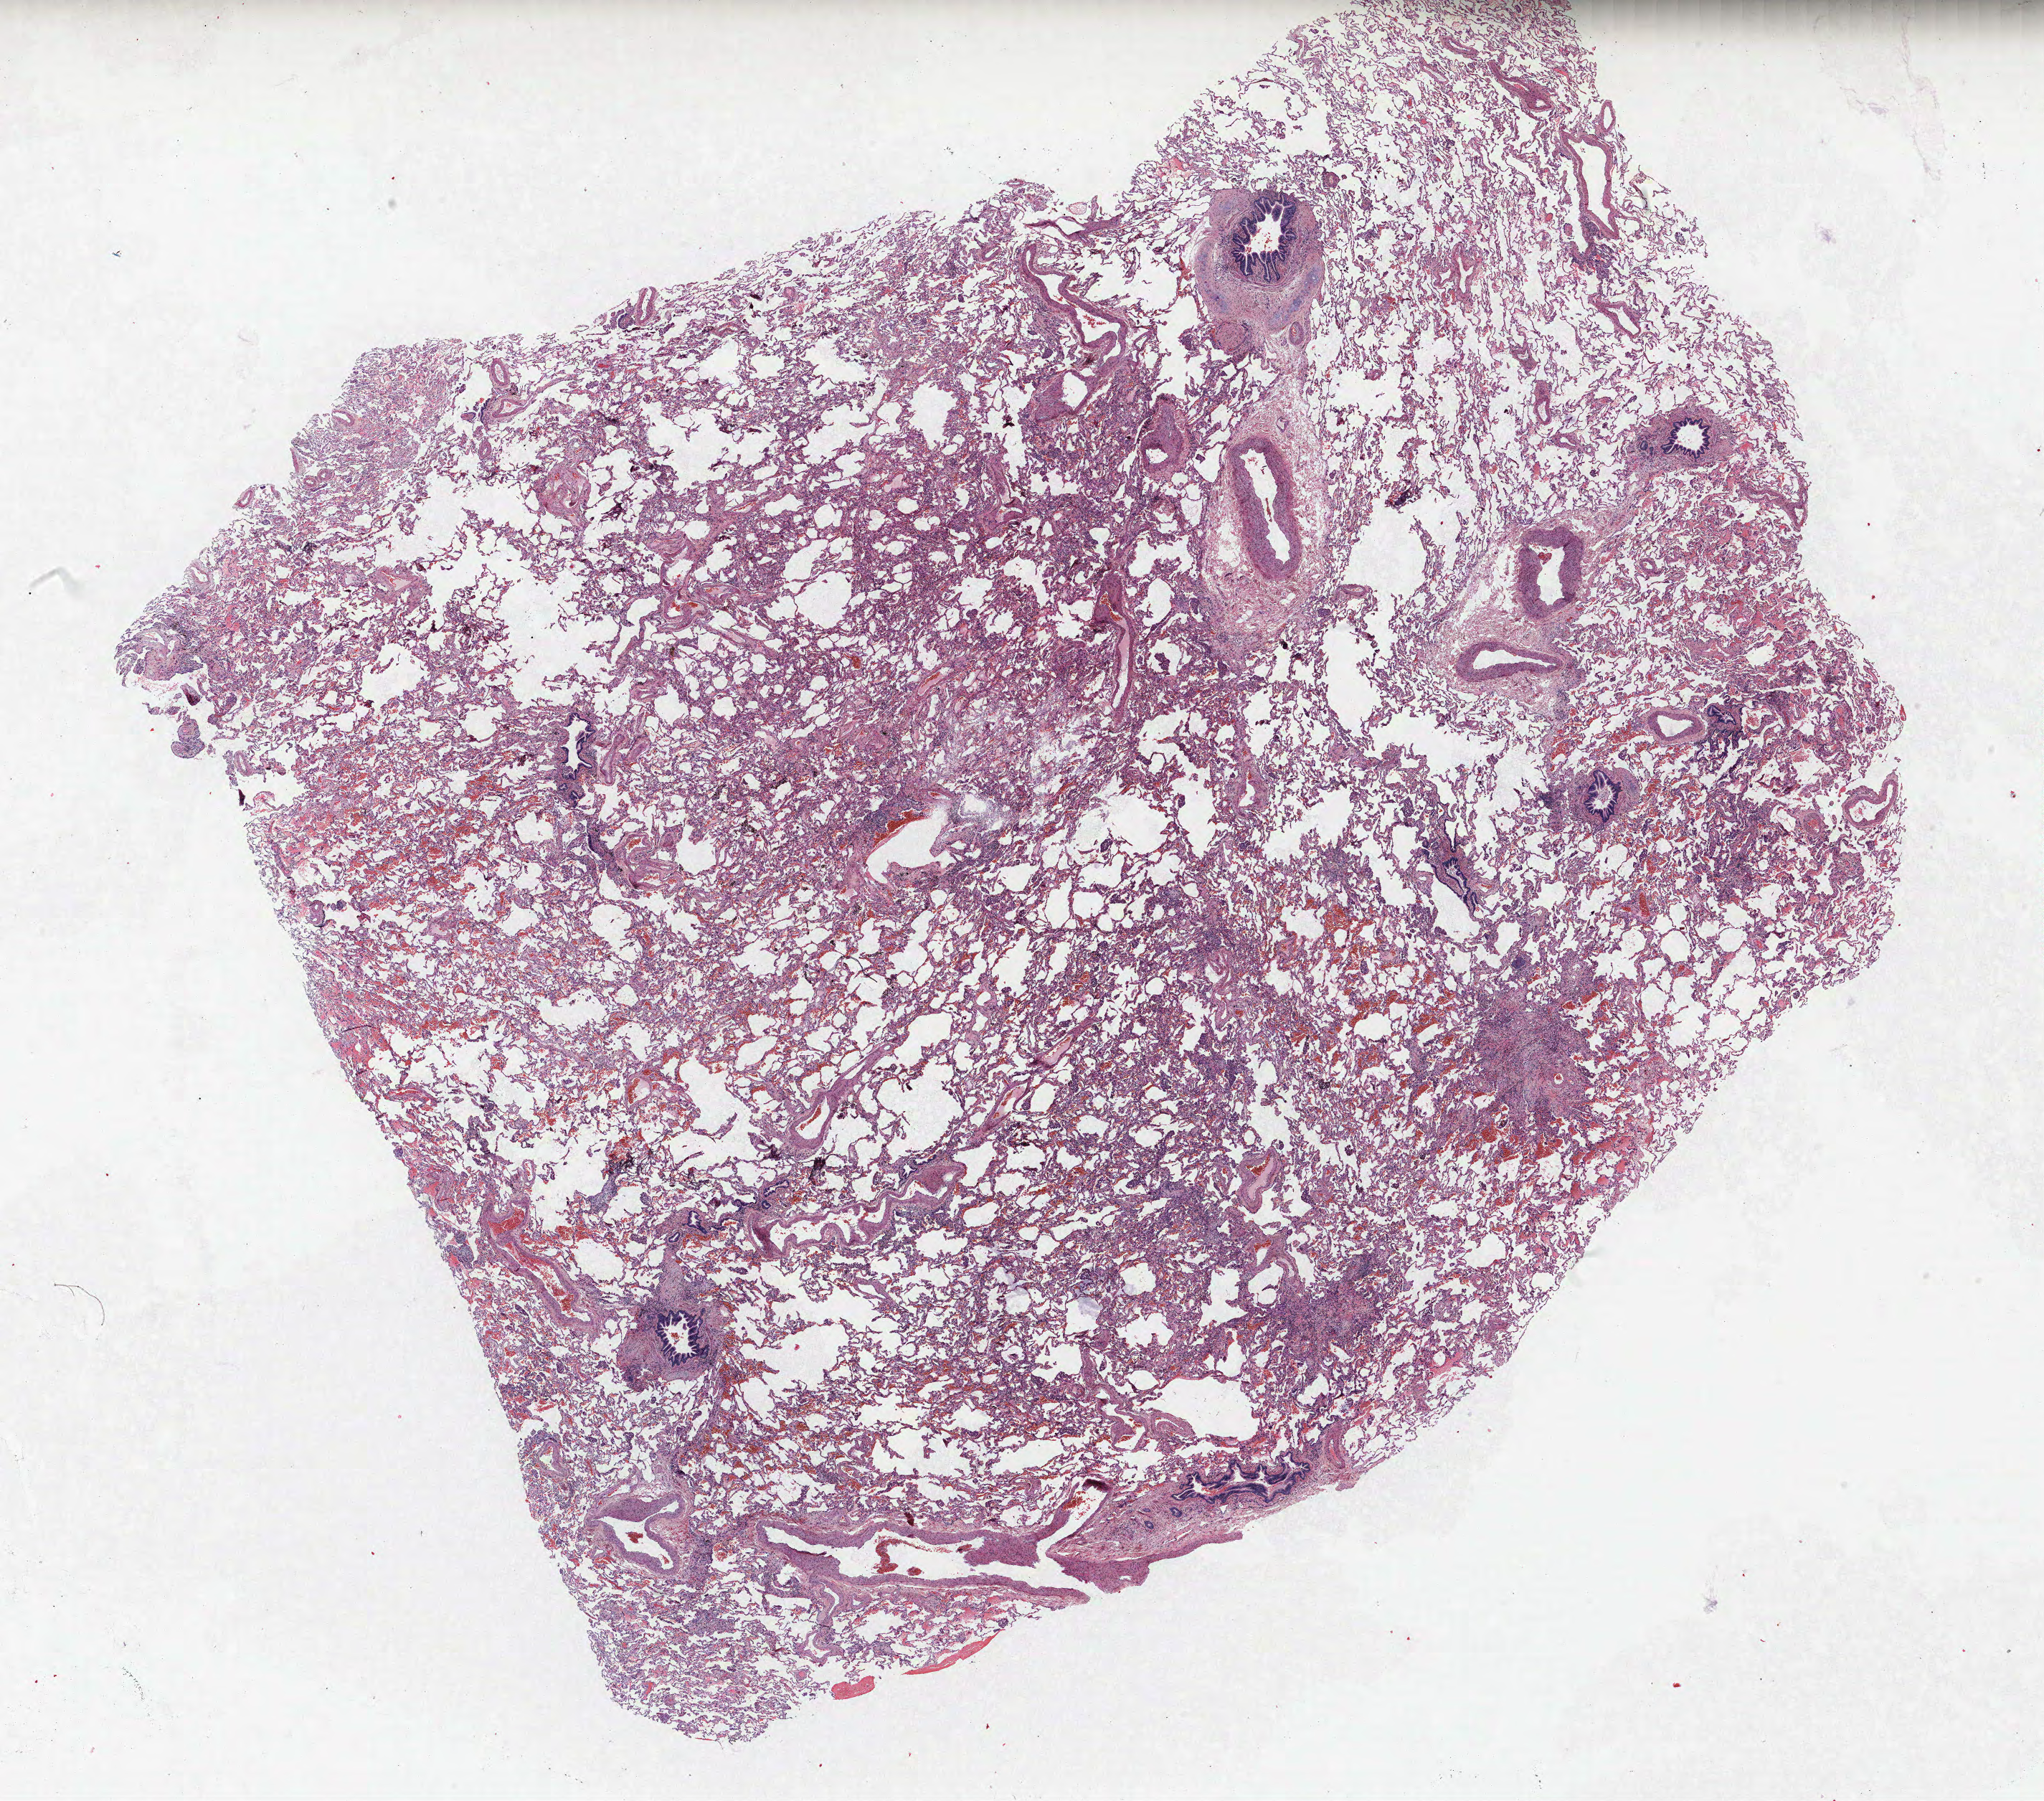
H&E-stained whole-slide image — low-resolution overview of the scanned area, about 22.8 x 20.1 mm (acquisition: 40x scan). Formalin-fixed paraffin-embedded (FFPE) section. Lung tissue. Male patient, aged 56 at enrolment. Current smoker at enrolment.
Participant's lung-cancer diagnosis: Large cell neuroendocrine carcinoma (ICD-O-3 8013/3).